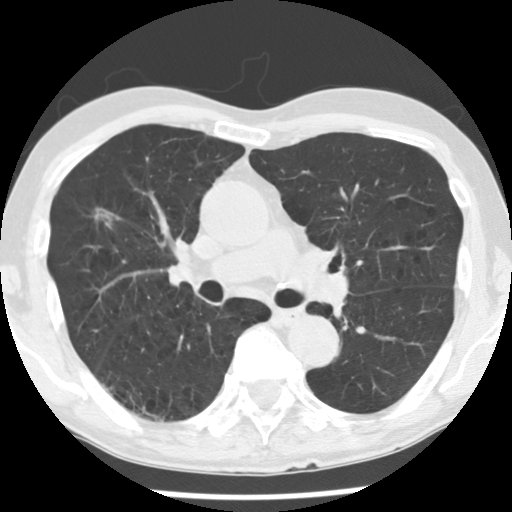
Low-dose screening chest CT, one axial slice; position 102 of 176 along the scan axis; reconstruction kernel STANDARD; lung window (W 1500 / L -600 HU); 2.5 mm slice thickness; 512 × 512 image matrix, field of view 309 × 309 mm.
Annotated regions visible in this slice (outlined manually by an expert reader):
- lesion 1 (tumor, upper lobe of right lung): bounding box (x1, y1, x2, y2) in pixels: (94, 208, 116, 228)